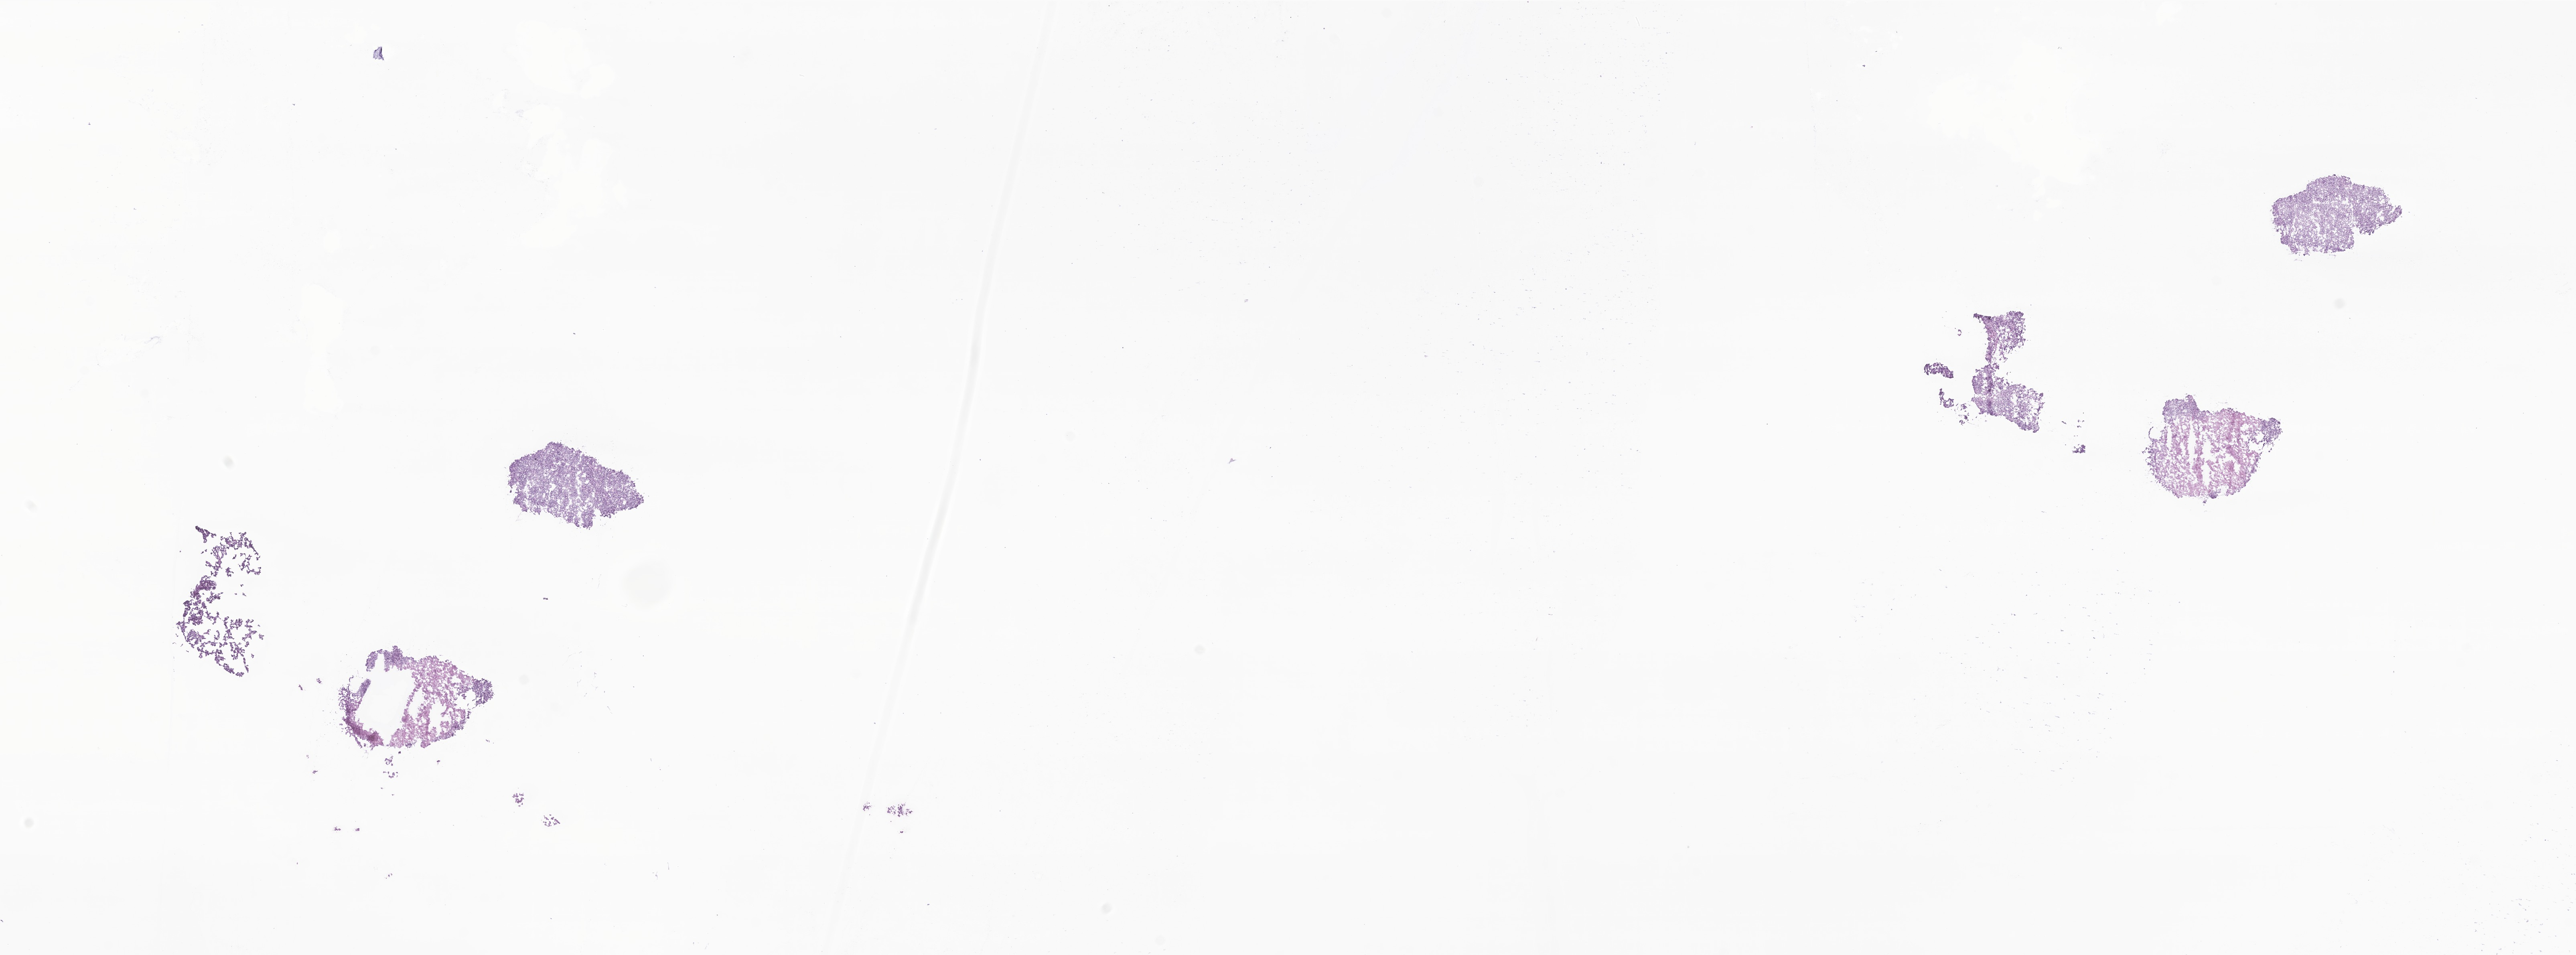
Whole-slide image, H&E stain of tumor tissue from the brain, a low-resolution overview of the entire scanned area, about 27.1 x 10.0 mm; frozen section. Female patient, age 641 days (about 1.8 years).
- recorded diagnosis: Neoplasm, uncertain whether benign or malignant